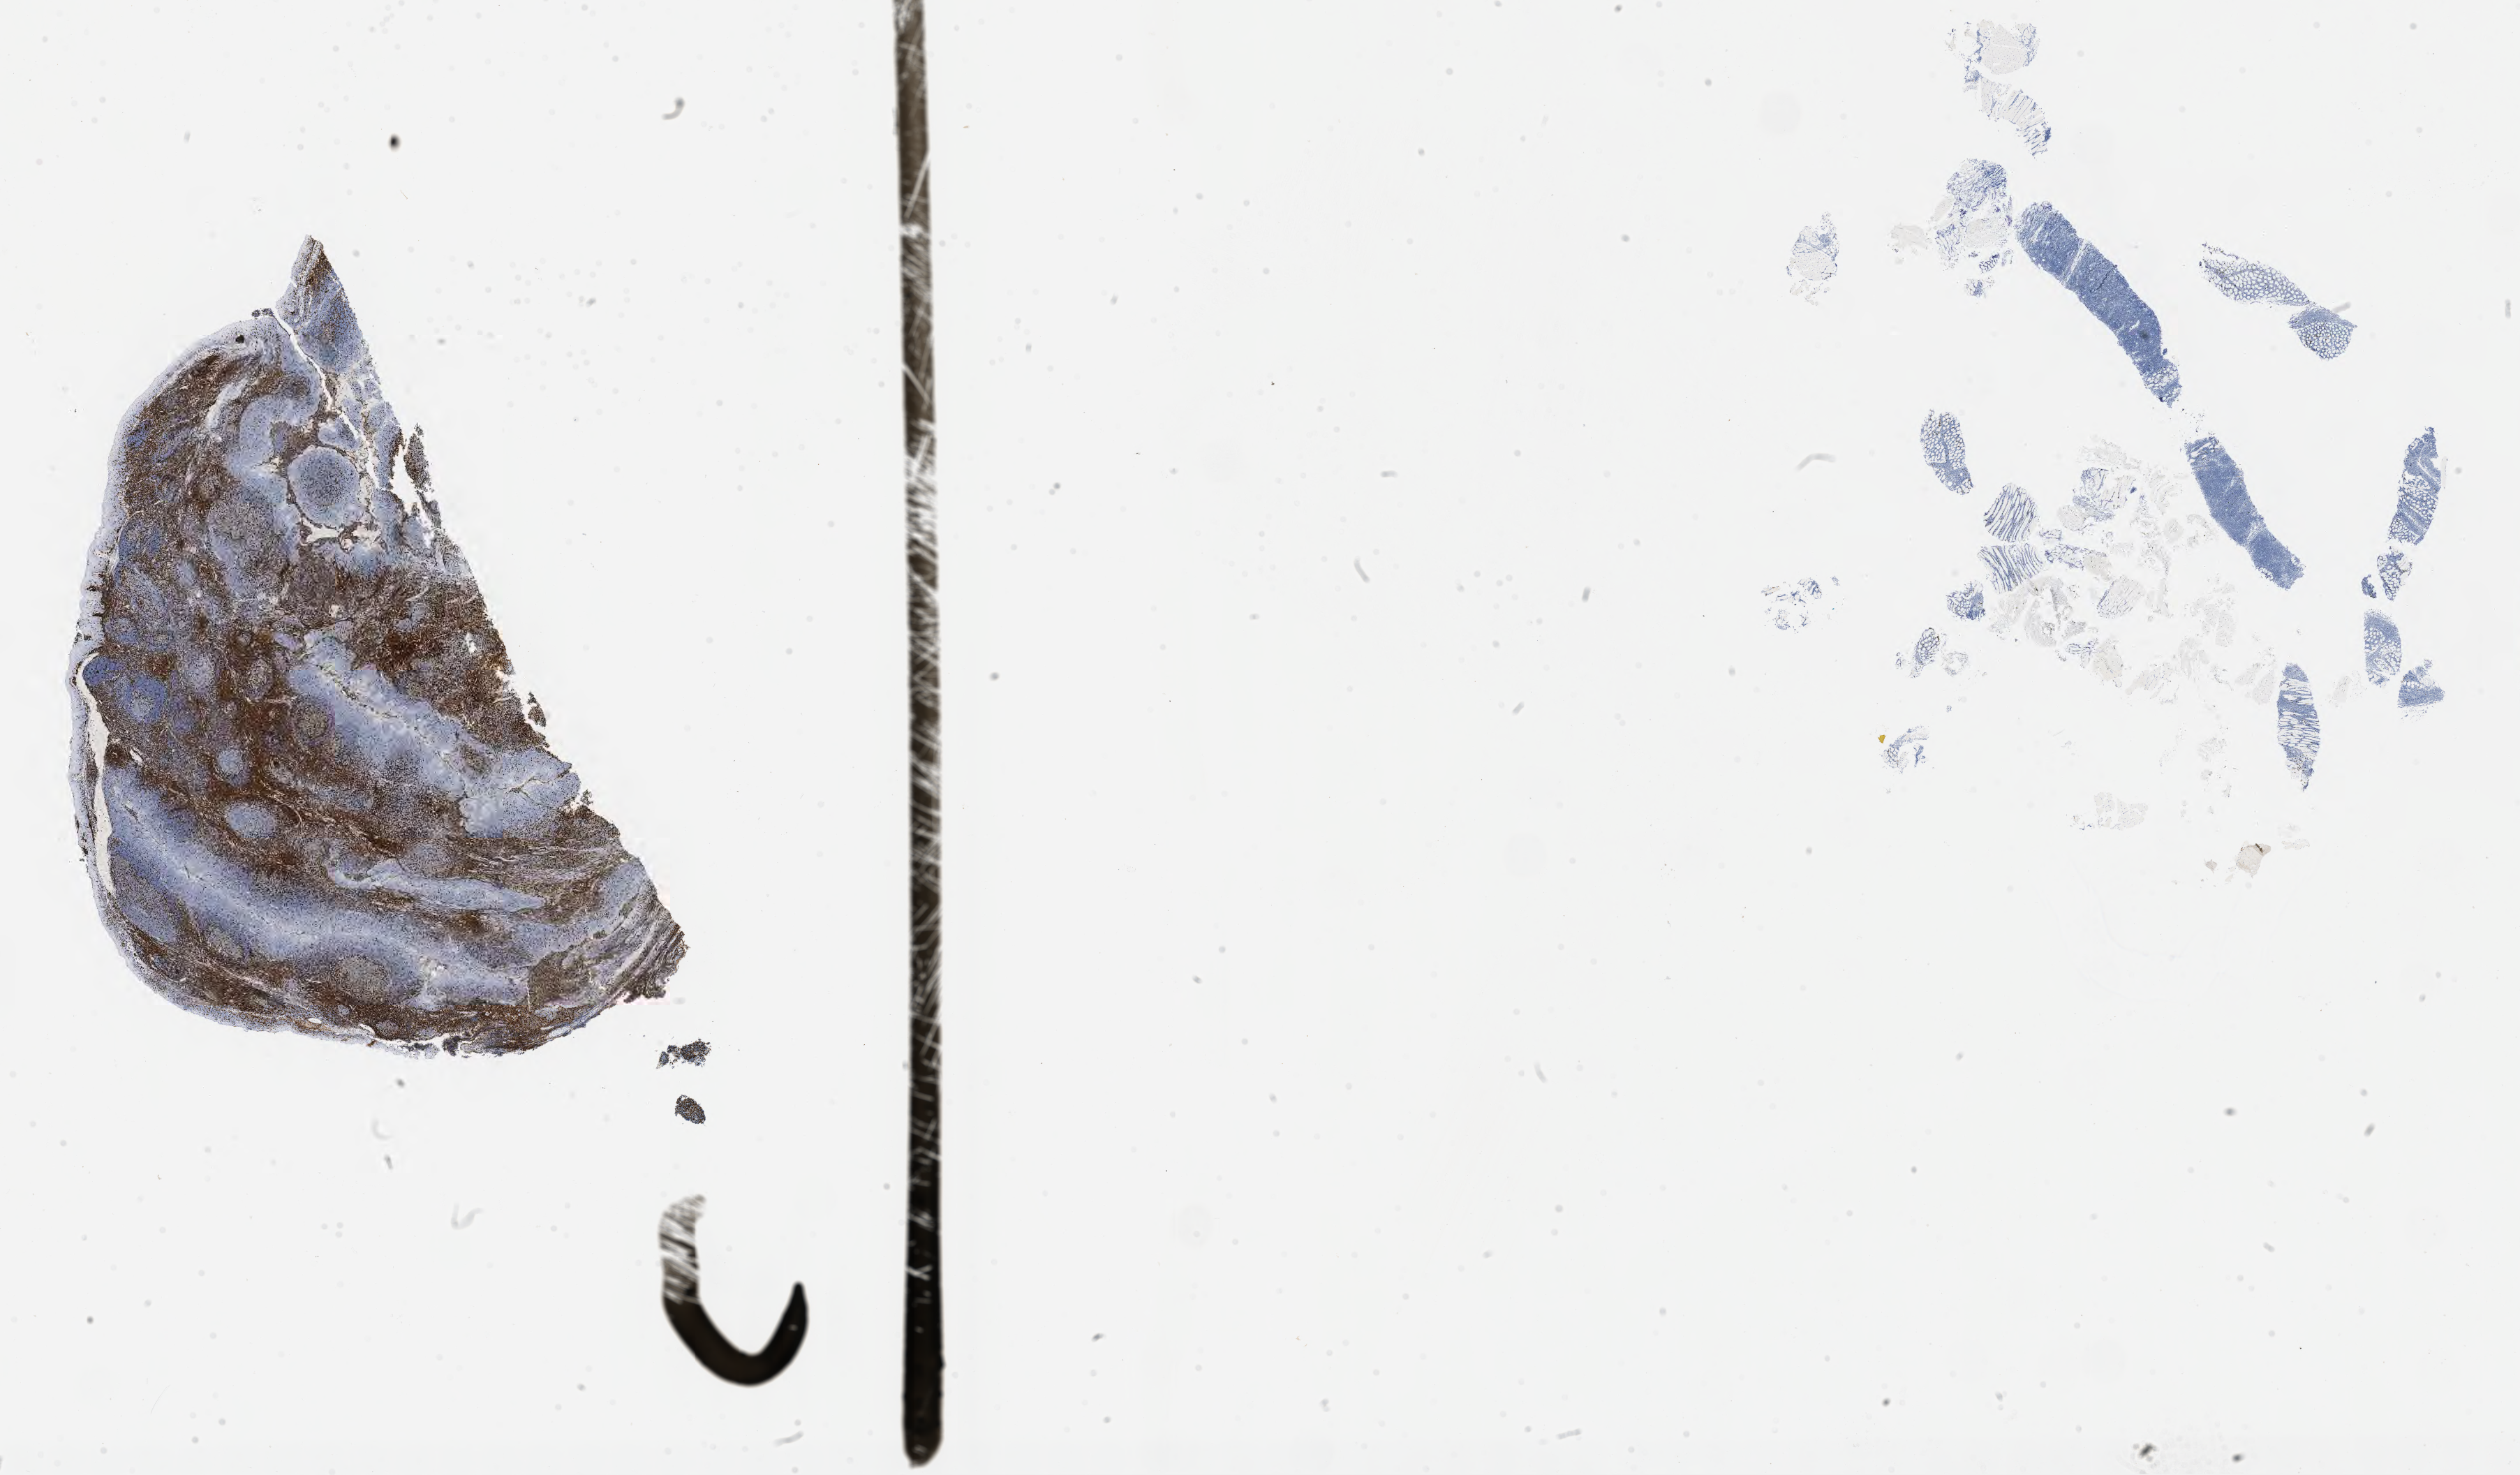
IHC for CD3, whole-slide image — a low-resolution overview of the entire scanned area, about 29.2 x 17.1 mm; specimen: tumor tissue; anatomic site: retroperitoneum. Patient: female, 53 years old.
- diagnosis: Burkitt lymphoma, NOS